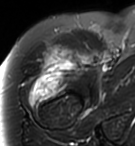
MRI of an extremity soft-tissue mass, one axial slice. Slice 80 of 95 in the series (ordered by position). T2-weighted fat-saturated. MR volume resampled by the dataset authors to the PET/CT grid (not the native acquisition matrix). 3.27 mm slice thickness. 135 × 146 image matrix, field of view 132 × 143 mm. Female patient. From the clinical record (not read from this slice): histological type: pleiomorphic undifferentiated sarcoma; grade: high; site of the primary tumour: right quadricep.
Annotated regions visible in this slice (expert contour drawn on MRI and transferred to this co-registered scan by the dataset authors):
- gross tumour volume including surrounding oedema: bounding box <28,45,90,108> (left, top, right, bottom; pixels)